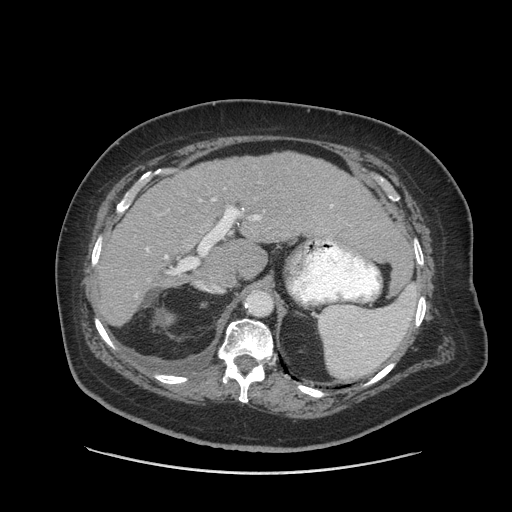
Contrast-enhanced abdominal CT (liver protocol), one axial slice. Reconstruction kernel STANDARD. 140 kVp. Soft-tissue window (W 400 / L 40 HU). 2.5 mm slice thickness. 512 × 512 image matrix, field of view 420 × 420 mm. From the clinical record (not read from this slice): diagnosis: hepatocellular carcinoma (patient treated with transarterial chemoembolisation; whether this scan precedes or follows treatment is not stated here); TNM stage (as recorded): Stage-I; Child-Pugh class: A; tumour differentiation: well differentiated; tumour nodularity: uninodular.
Outlined on this slice (semi-automatic segmentation, software-assisted and operator-edited):
- liver parenchyma outside the tumour (the mass and vessels are separate outlines, so this box may not span the whole liver): bounding box (x1, y1, x2, y2) in pixels: (96, 152, 399, 324)
- liver vessels: (146, 199, 260, 251)